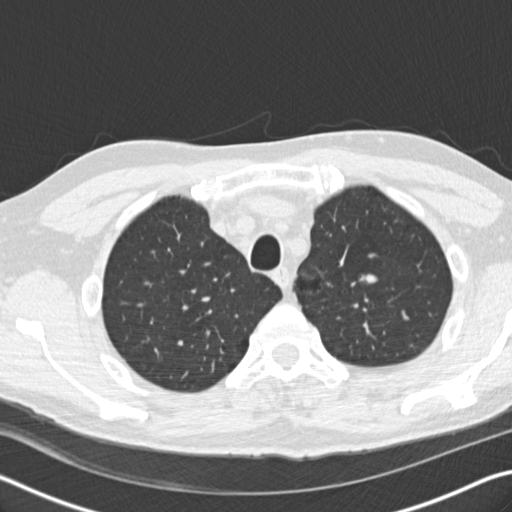
Axial slice from a low-dose chest CT screening exam; baseline annual screen; lung window (W 1500 / L -600 HU); 2 mm slice thickness; slice 39 of 208 in the series; 512 × 512 image matrix. Male participant, aged 56 years at enrolment. Current smoker at enrolment.
Lesion marked by an expert reader, bounding box [x1, y1, x2, y2] px = [343, 261, 389, 300]. Reader record for this screening exam (exam-level; its link to the box is not recorded): non-calcified nodule or mass ≥4 mm, left upper lobe, 12 × 10 mm, smooth margins, soft tissue attenuation. Official screen result: positive, change unspecified: nodule(s) >= 4 mm or enlarging nodule(s), mass(es), or other non-specific abnormalities suspicious for lung cancer. Lung cancer was diagnosed 814 days after this screen: neuroendocrine carcinoma, NOS, left upper lobe, well differentiated (G1), stage IA (AJCC 6th edition), 20 mm at pathology.